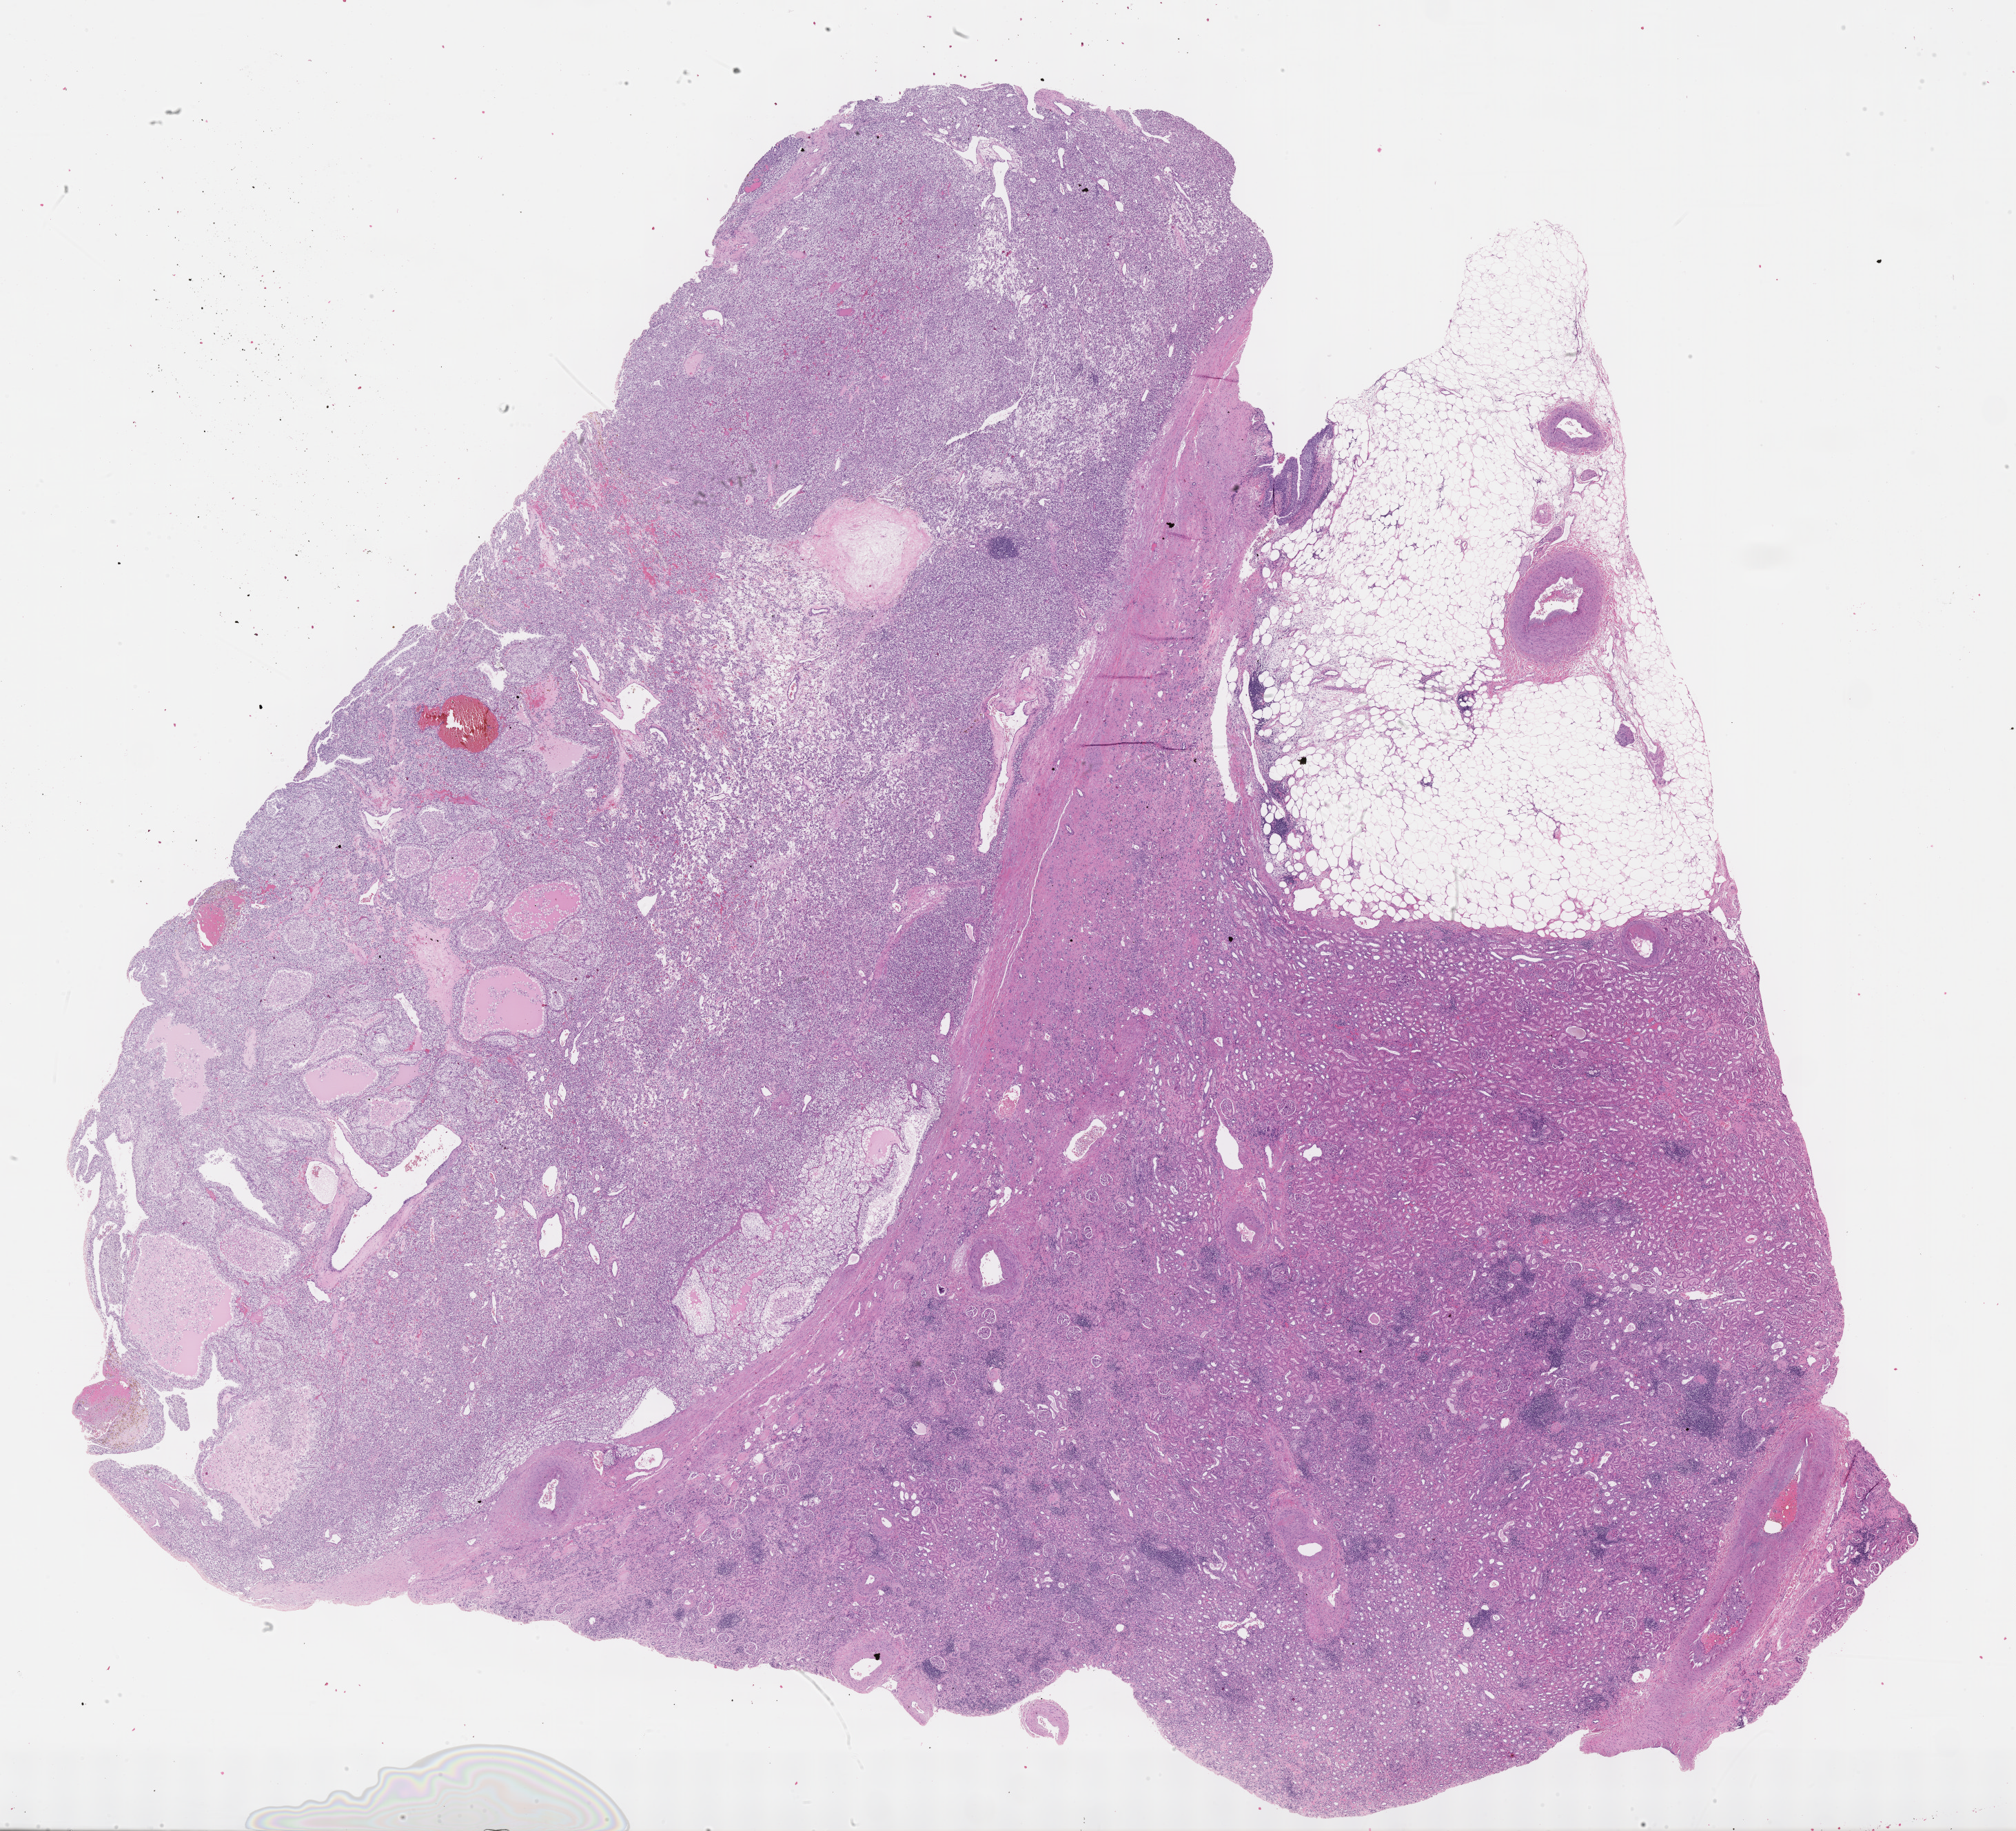
Whole-slide histology image, H&E — a low-resolution overview of the entire scanned area, about 23.6 x 21.5 mm, FFPE section, primary tumour sample from the kidney. Patient: male, age at initial diagnosis 65 years. Histologic grade: G3 (poorly differentiated).
AJCC pathologic stage: I (6th edition). Histologic diagnosis: Clear cell adenocarcinoma, NOS. Lymph nodes positive (case pathology): 0 of 11 examined.